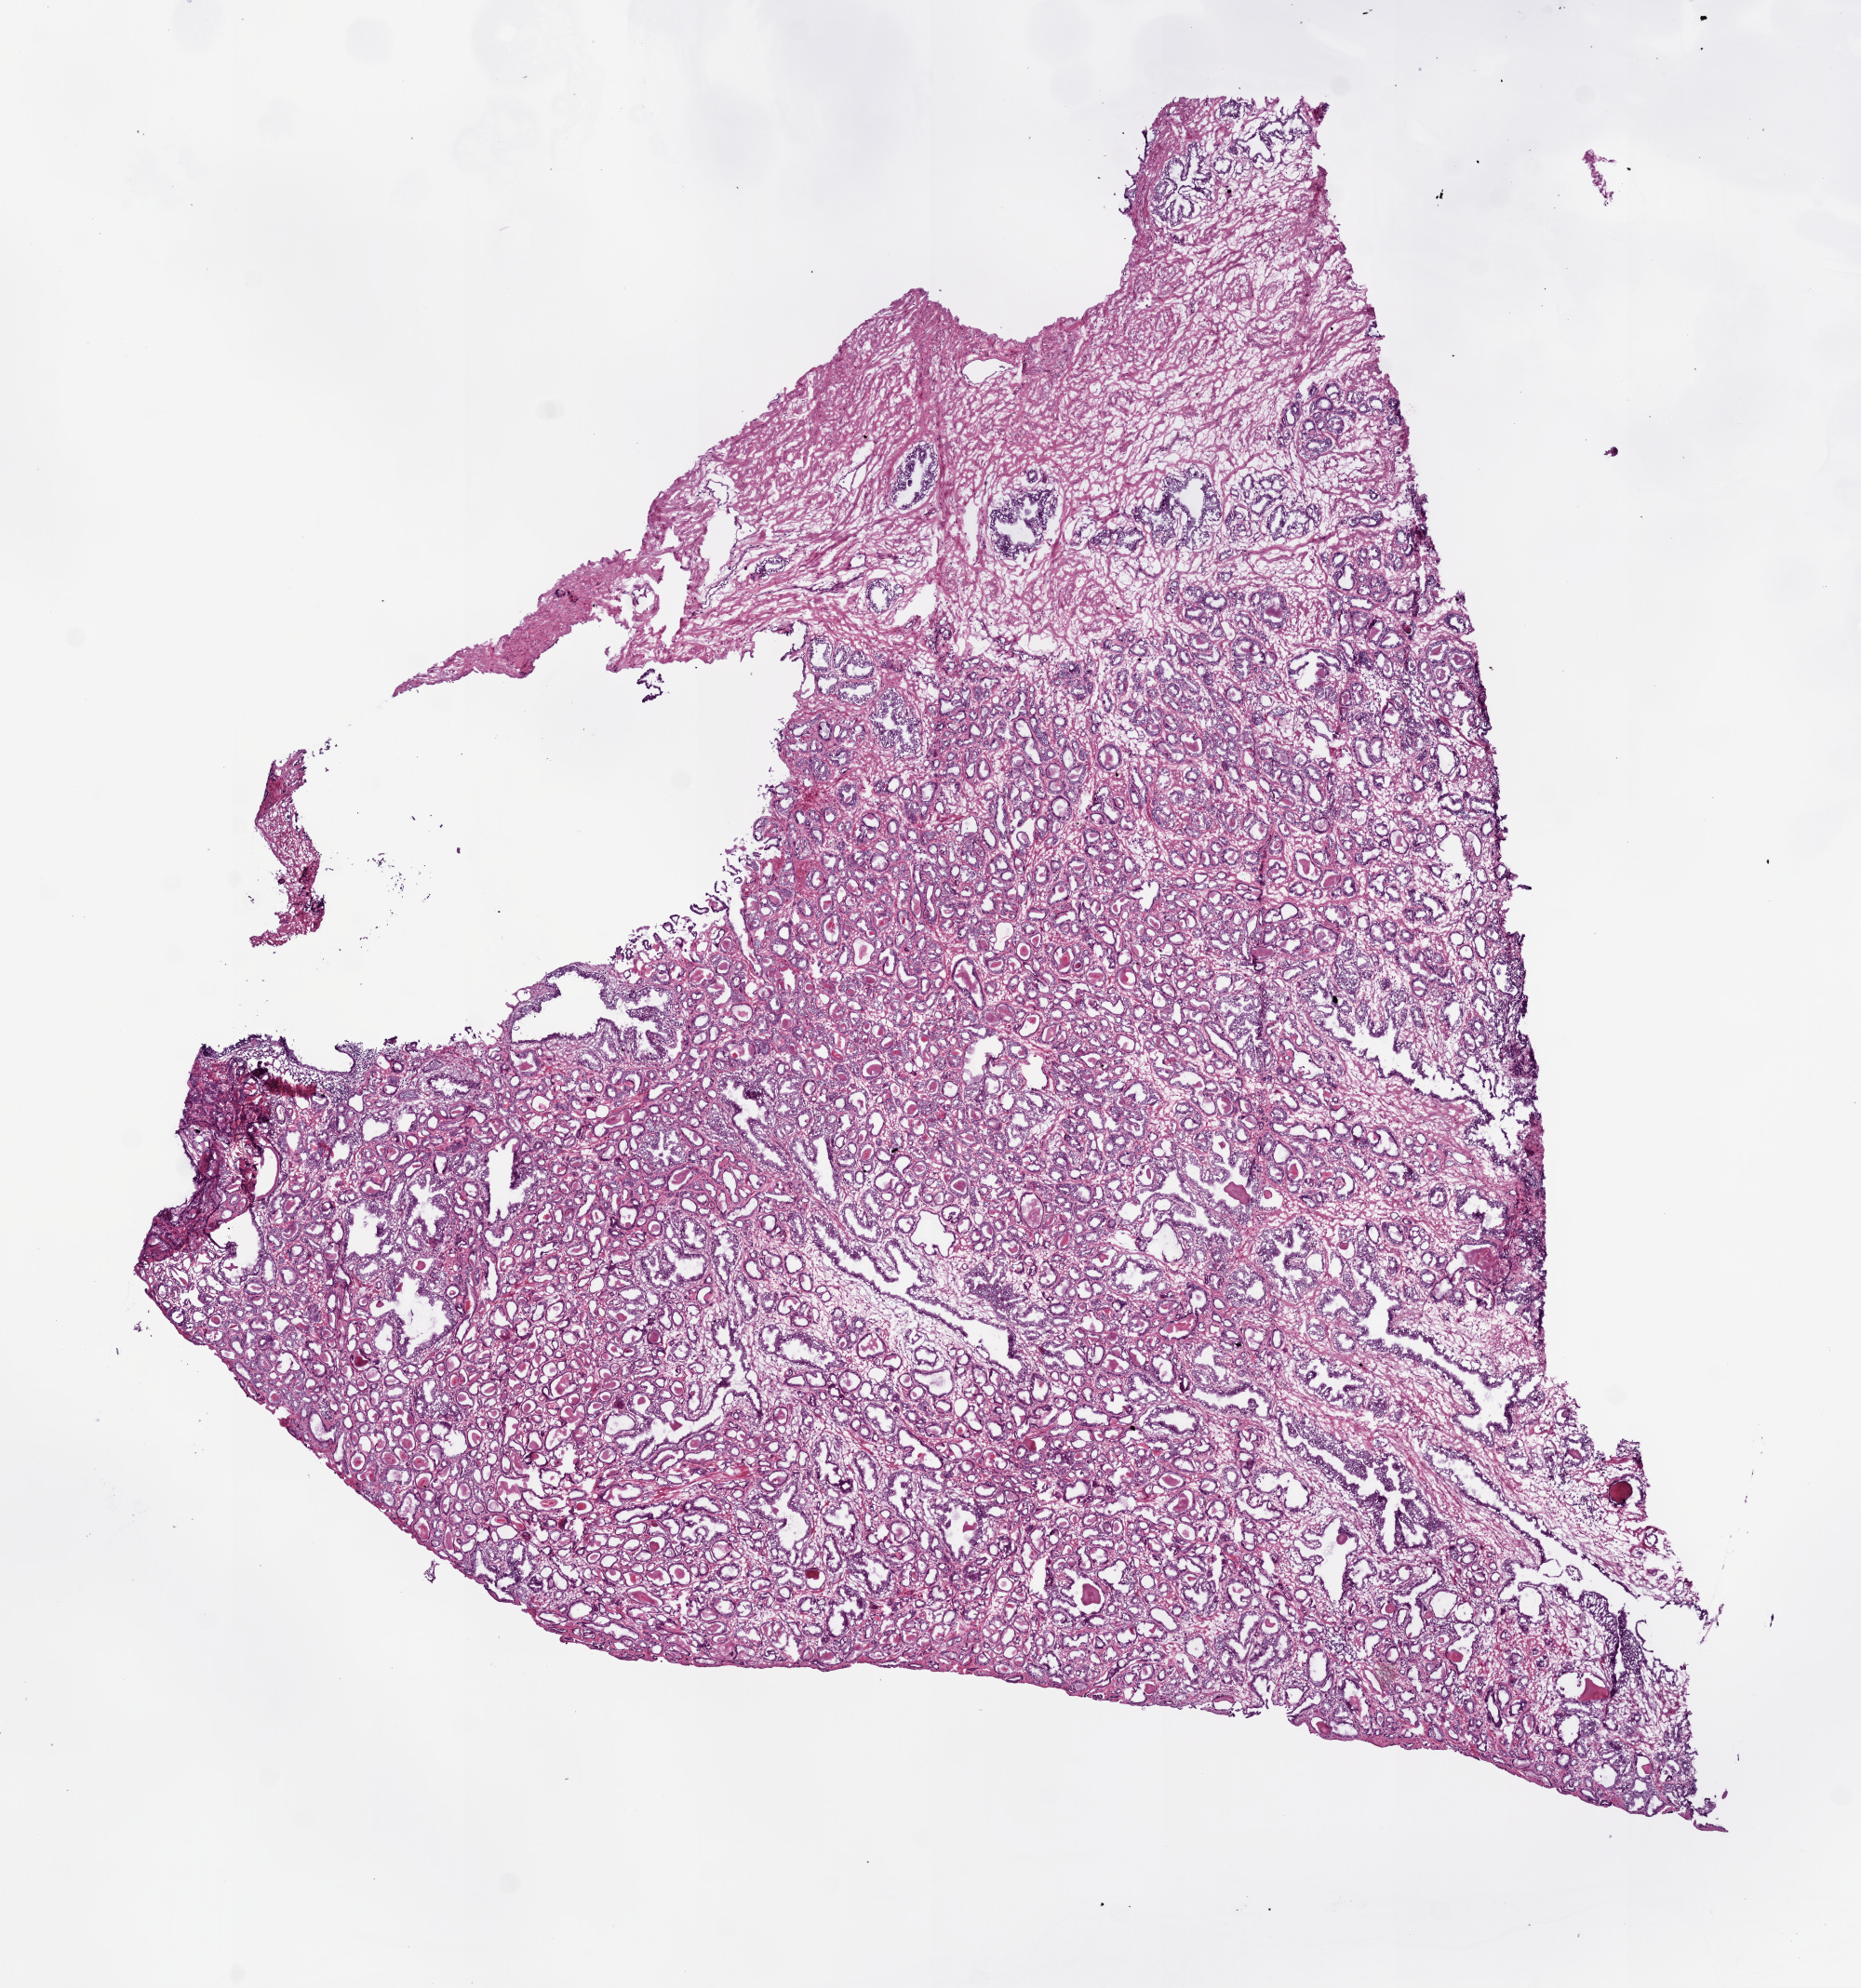
Whole-slide histology image, H&E, shown as a low-resolution overview of the whole scanned area (about 8.0 x 8.6 mm, slide scanned at 20x); frozen section; sample: primary tumour, prostate. Male, age 46 years at initial diagnosis. Gleason score: 7 (3+4). Slide review estimates, as recorded: tumour cells 60%, tumour nuclei 75%, normal cells 15%, stromal cells 25%, necrosis 0%. Inflammatory infiltration, as recorded: lymphocyte infiltration 1%, monocyte infiltration 0%, neutrophil infiltration 0%.
Pathologic diagnosis: Acinar cell carcinoma (prostate gland). Lymph nodes positive (case pathology): 0 of 13 examined.